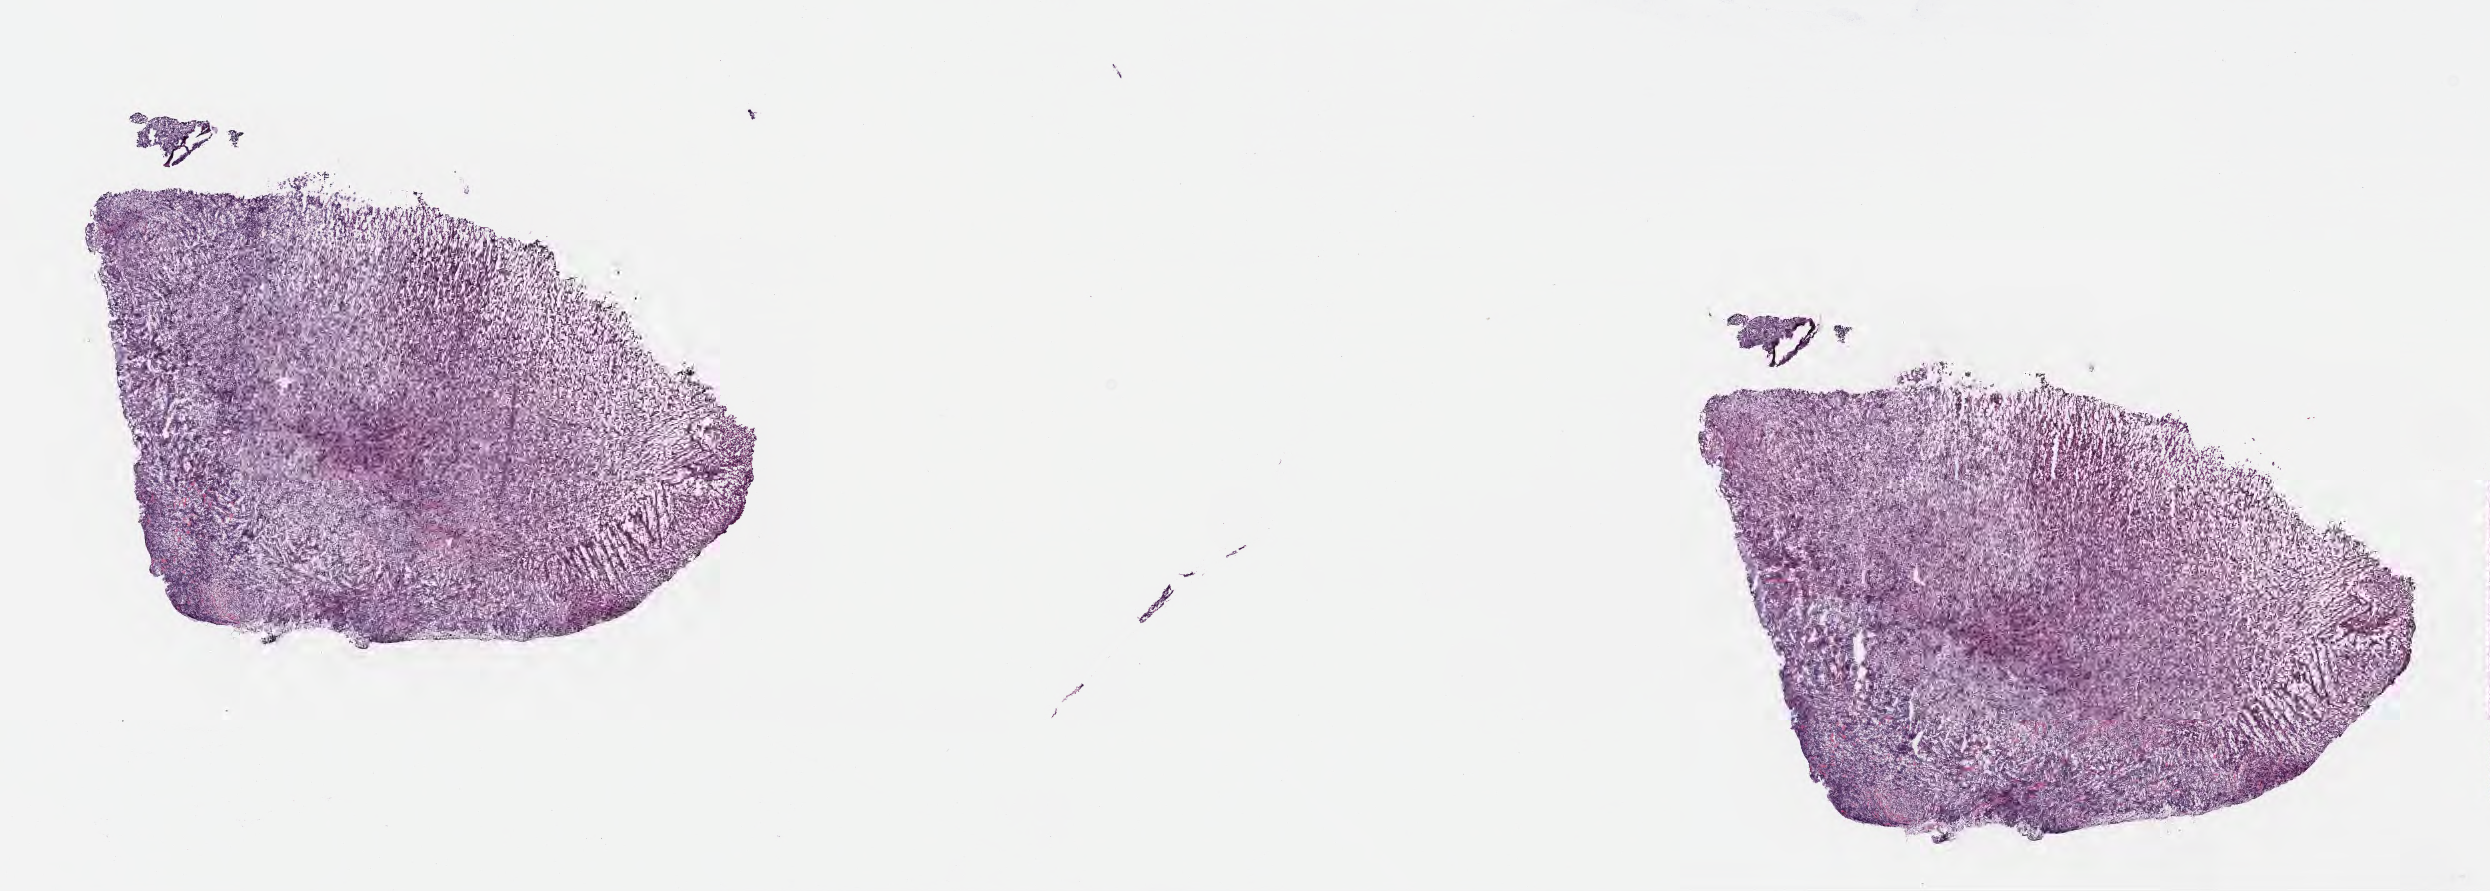
Digitized haematoxylin and eosin-stained section, low-resolution overview of the scanned area, about 20.1 x 7.2 mm, frozen section (tissue freezing medium), specimen: primary tumor, site: lip. Male patient; age at initial diagnosis 7 years. Slide review estimates, as recorded: tumor cells 85%, tumor nuclei 85%, stromal cells 10%, necrosis 5%, normal cells 0%. Inflammatory infiltration, as recorded: lymphocyte infiltration 50%, monocyte infiltration 30%, neutrophil infiltration 5%.
Diagnosis: Diffuse large B-cell lymphoma, NOS. Section: top of the tissue portion. Ann Arbor stage (patient): Stage II.